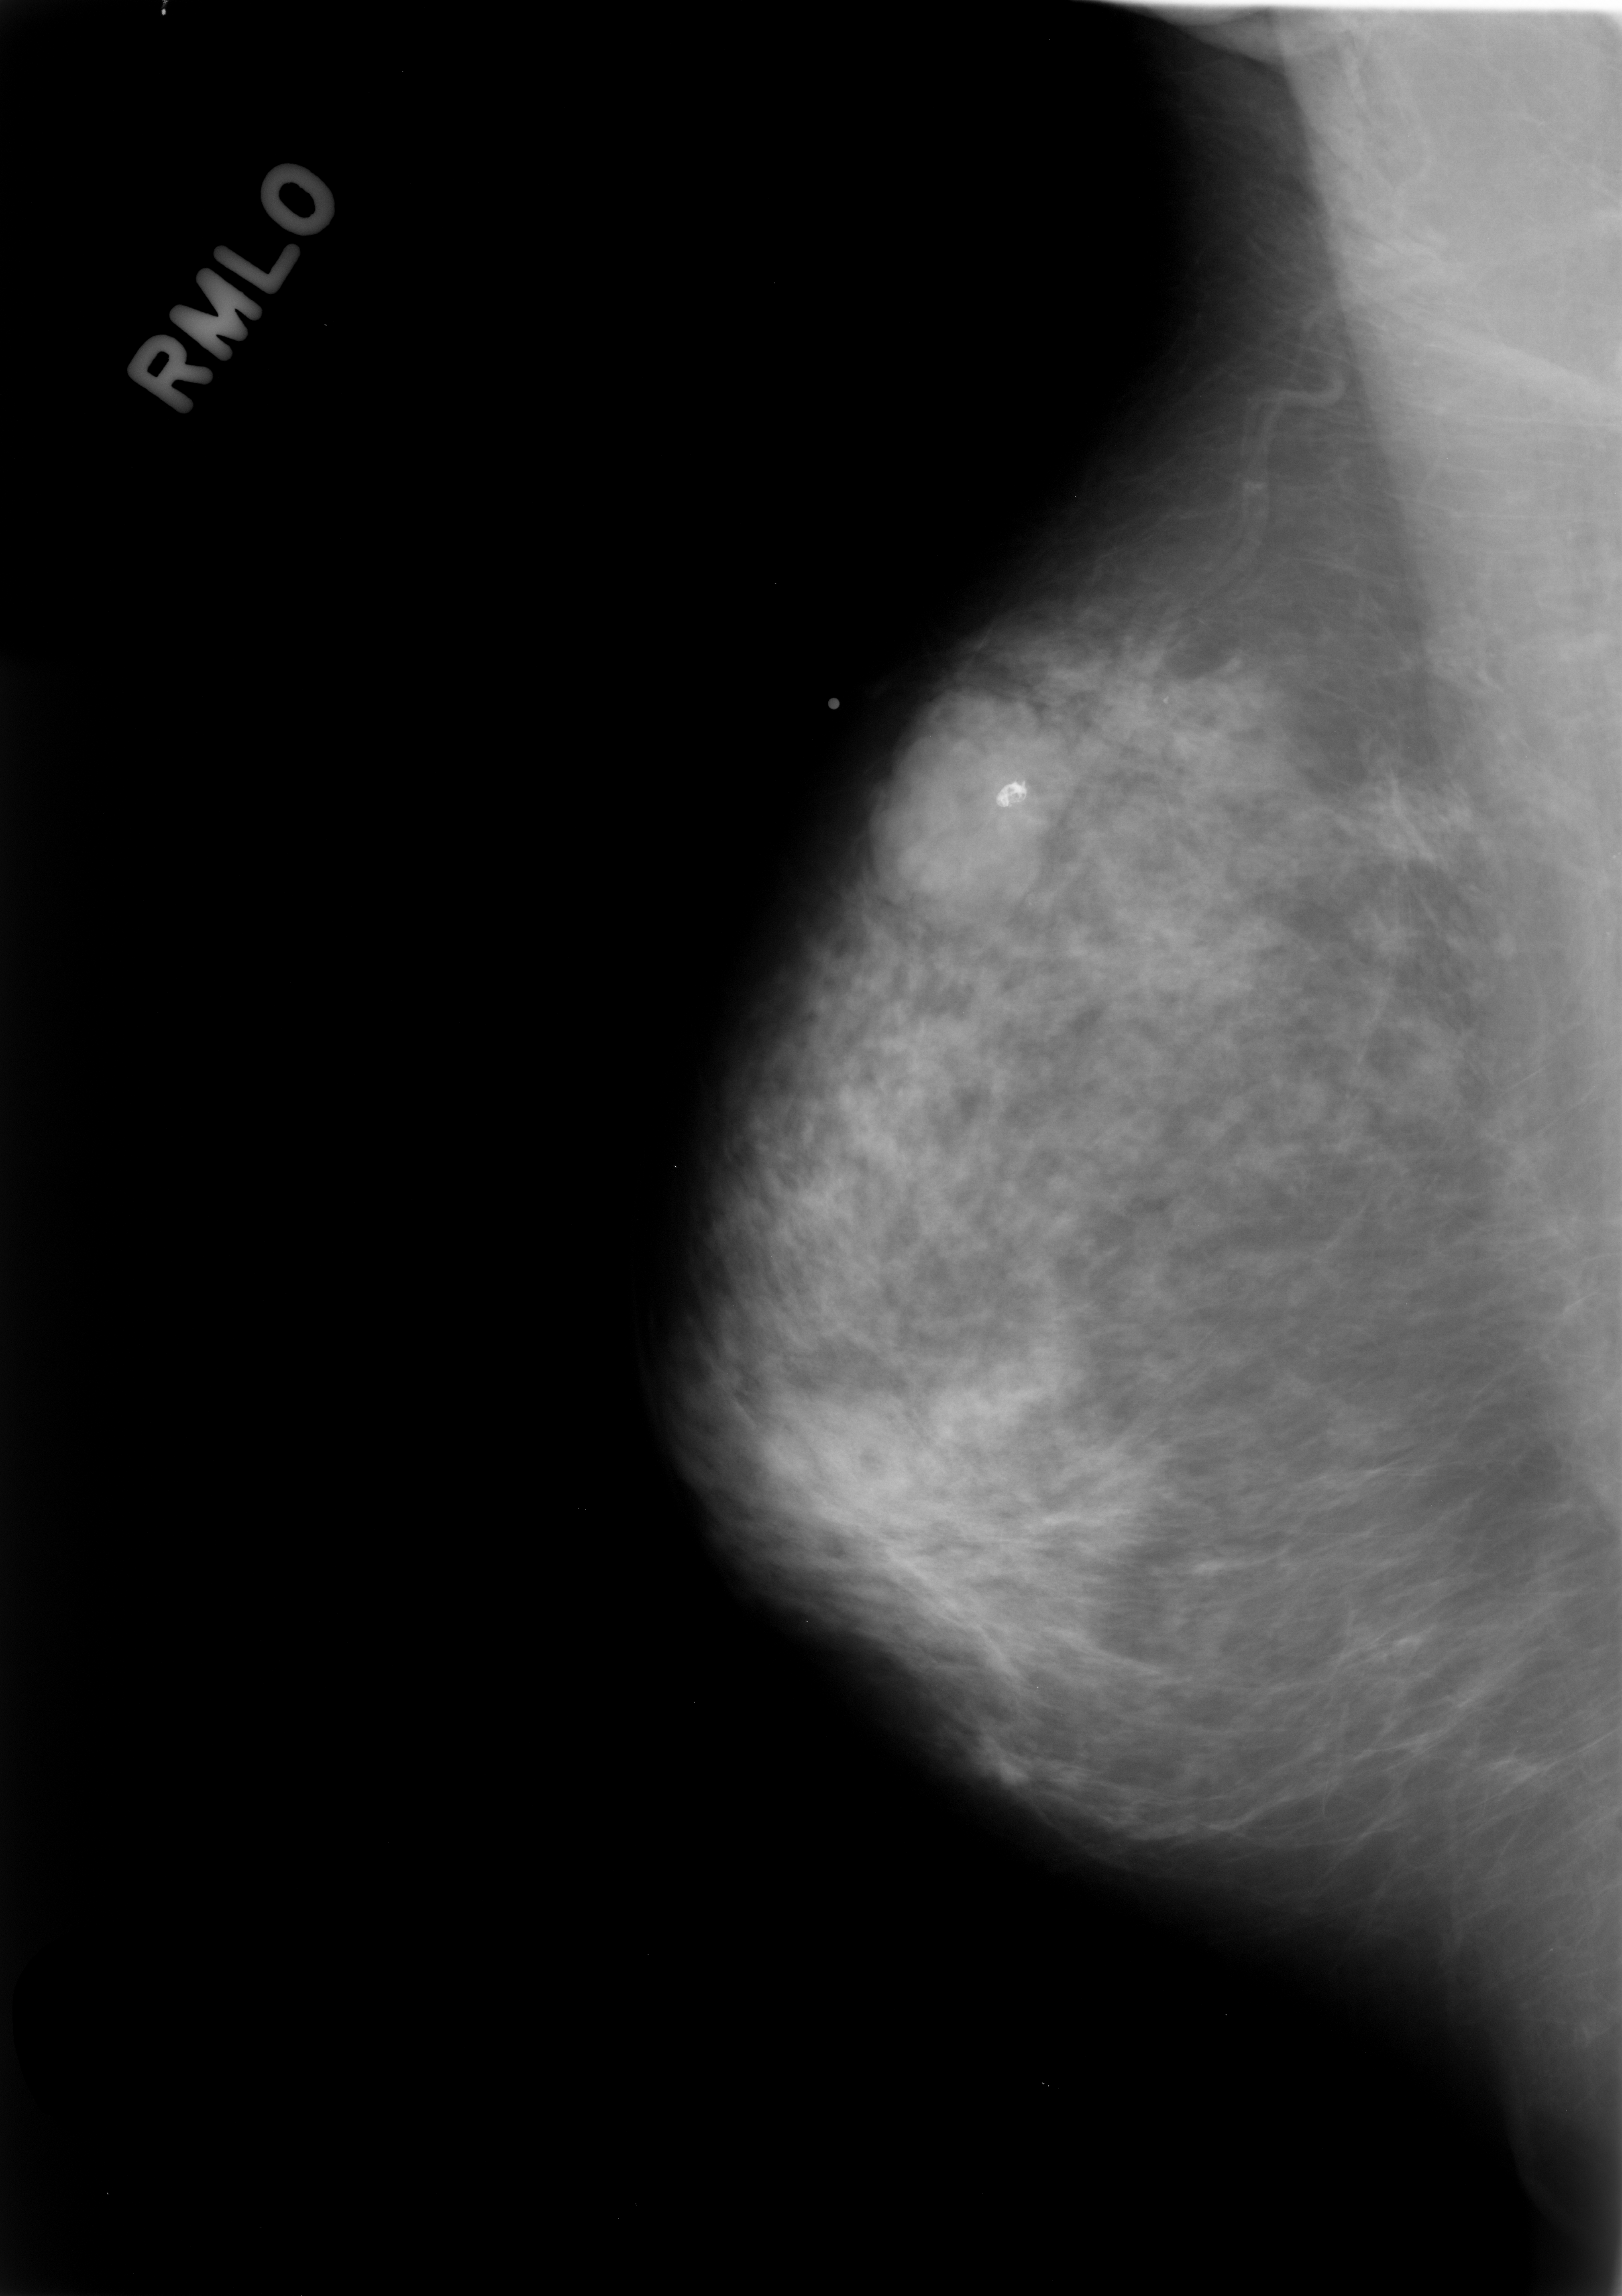
Scanned film-screen mammogram; right breast; MLO view; 1622 × 2296 image matrix.
Expert-marked regions of interest on this image (one box per marked abnormality):
- mass, shape lobulated, margins microlobulated; BI-RADS assessment category 4; pathology (as recorded): benign: bounding box [x1, y1, x2, y2] px = [871, 686, 1070, 935]